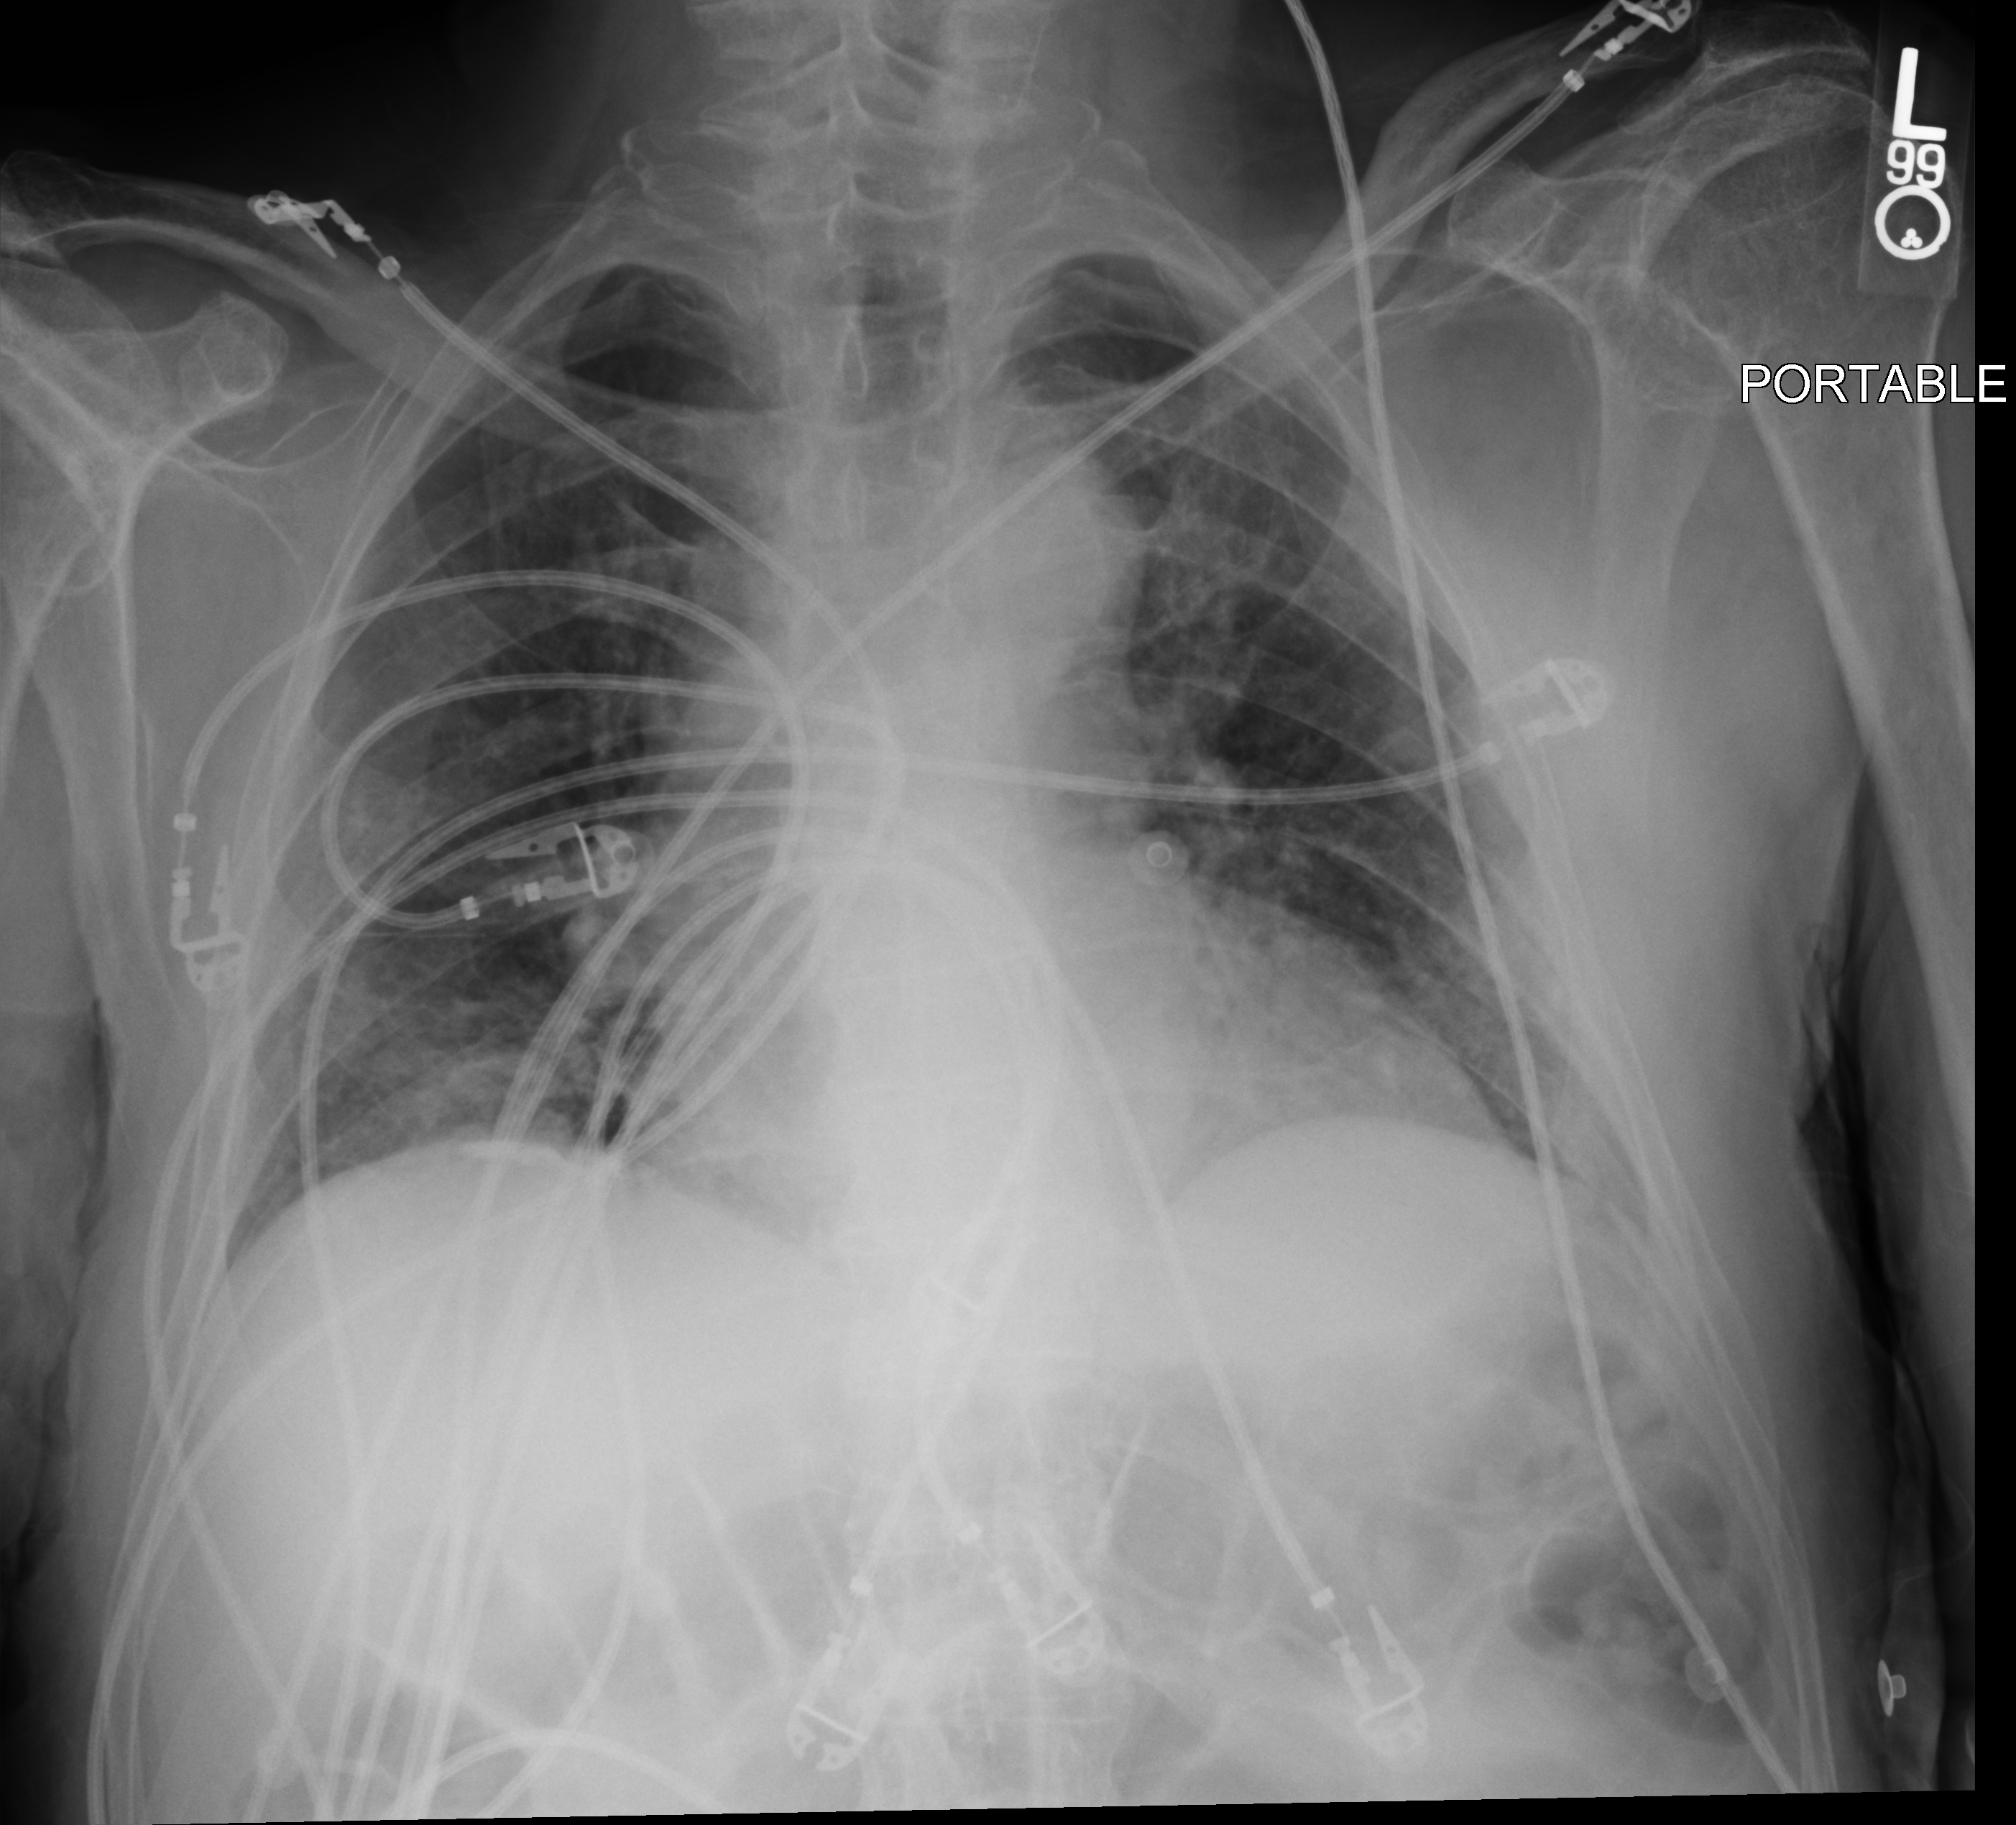
Chest X-ray (portable). Male patient hospitalised with COVID-19, age 75–90 years.
Hospital-stay facts (about this admission, not read from this image; timing relative to this image not recorded): admitted to intensive care during this hospital stay: no; mechanically ventilated during this hospital stay: no.